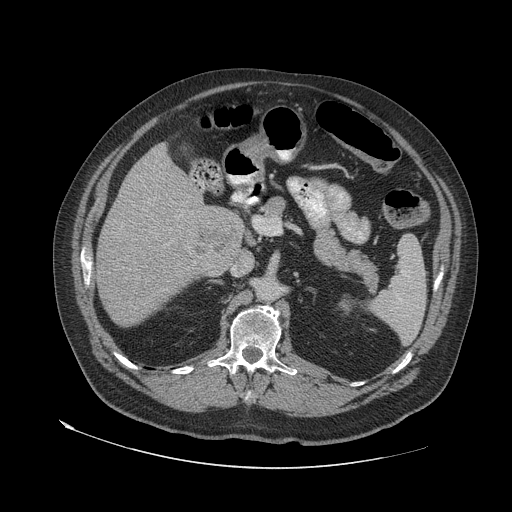
Contrast-enhanced abdominal CT (liver protocol), one axial slice; position 29 of 79 along the scan axis; reconstruction kernel STANDARD; 140 kVp; soft-tissue window (W 400 / L 40 HU); 2.5 mm slice thickness; 512 × 512 image matrix. From the clinical record (not read from this slice): diagnosis: hepatocellular carcinoma (patient treated with transarterial chemoembolisation; whether this scan precedes or follows treatment is not stated here); TNM stage (as recorded): Stage-IVA; Child-Pugh class: A; tumour differentiation: well differentiated.
Outlined on this slice (semi-automatically segmented with operator editing):
- liver parenchyma outside the tumour (the mass and vessels are separate outlines, so this box may not span the whole liver): bounding box (x1, y1, x2, y2) in pixels: (96, 144, 244, 324)